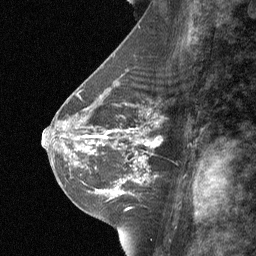
Breast MRI (dynamic contrast-enhanced), one sagittal slice. Position 33 of 64 along the scan axis. Dynamic contrast-enhanced study with each time point stored as its own series, time point 2 of 3 at this slice position (early post-contrast, ordered by acquisition time). 1.5 T. TE 4.8 ms, TR 27 ms. 256 × 256 image matrix, field of view 180 × 180 mm. Patient: female, 42 years. Case-level facts recorded for this patient, not image findings: setting: breast cancer imaged before/during neoadjuvant chemotherapy; receptor status: triple-negative.
Annotated regions visible in this slice (semi-automatic segmentation, software-assisted and operator-edited):
- analysis volume of interest (the breast-tissue region the enhancement analysis was run in; not a lesion): bounding box [x1, y1, x2, y2] px = [99, 117, 165, 187]
- tumour enhancement mask (voxels above the 90 % enhancement threshold inside the analysis volume of interest): [131, 121, 161, 181]